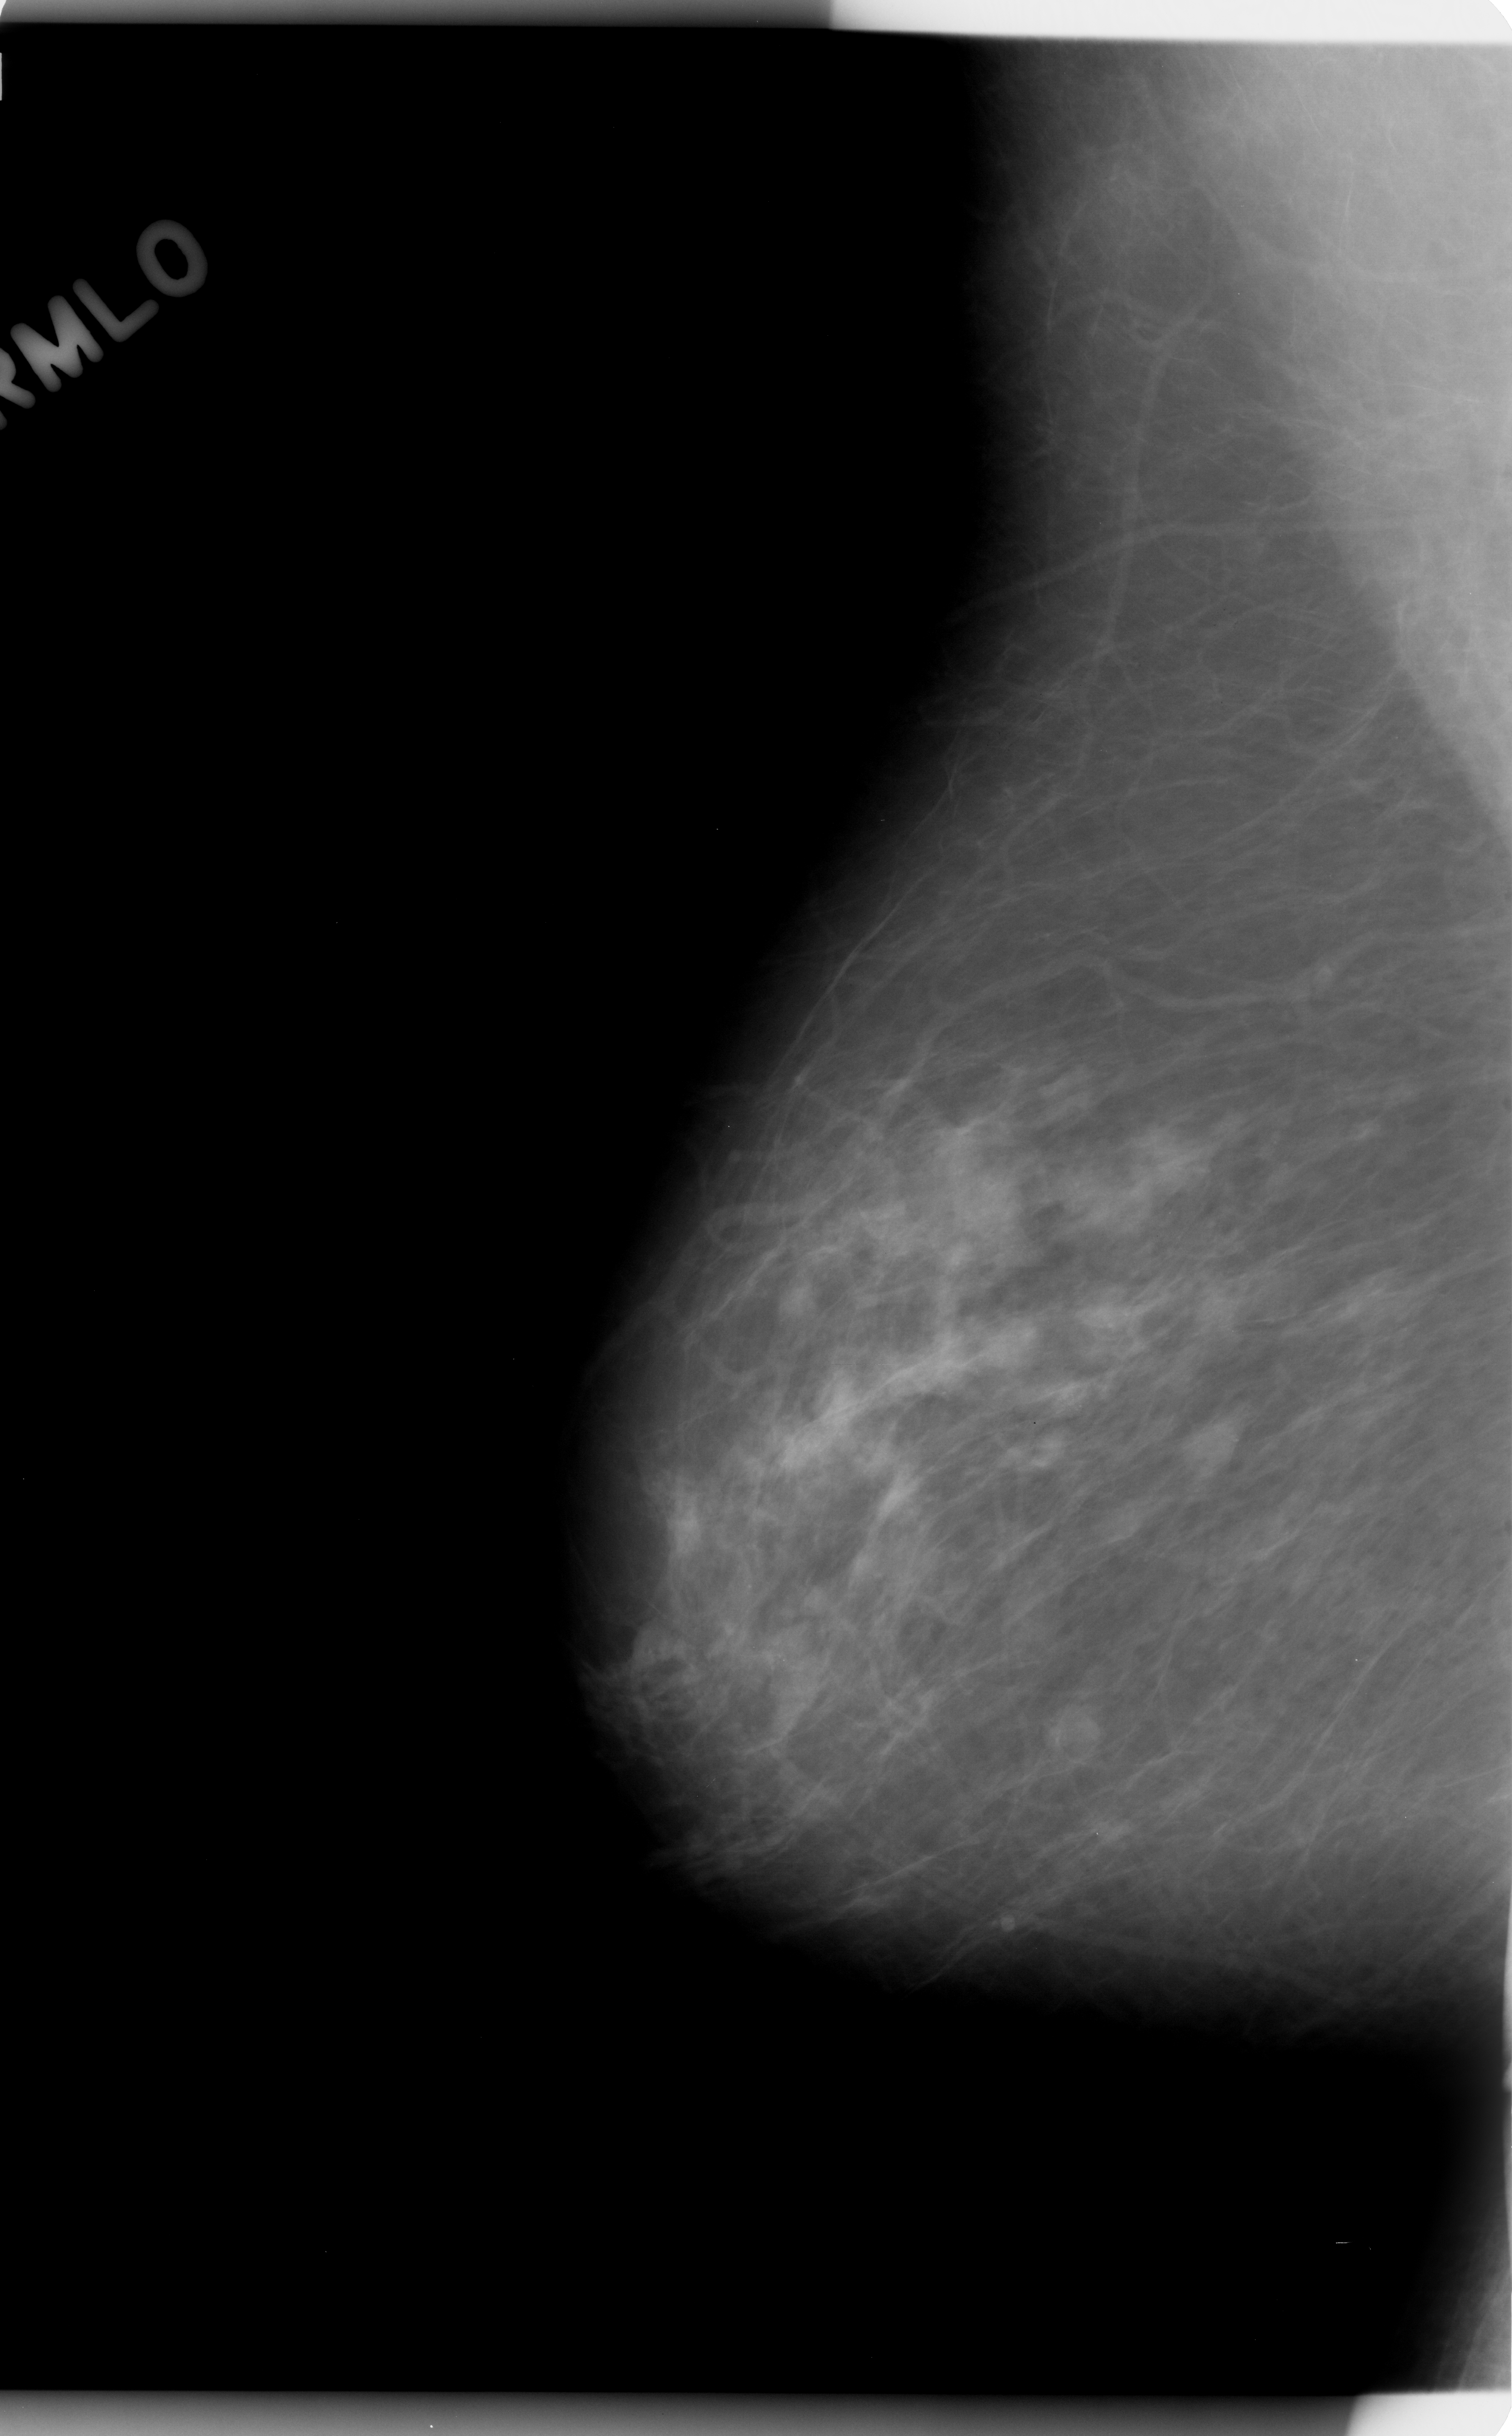
Mammogram (digitized film); right breast; MLO view; 1512 × 2436 image matrix.
Marked abnormalities (boxes around the expert regions of interest):
- calcifications, morphology amorphous, distribution regional; BI-RADS assessment category 4; subtlety rating 2 on a 1 (subtle) to 5 (obvious) scale; pathology (as recorded): benign: box from (x=690, y=1130) to (x=1188, y=1750) px